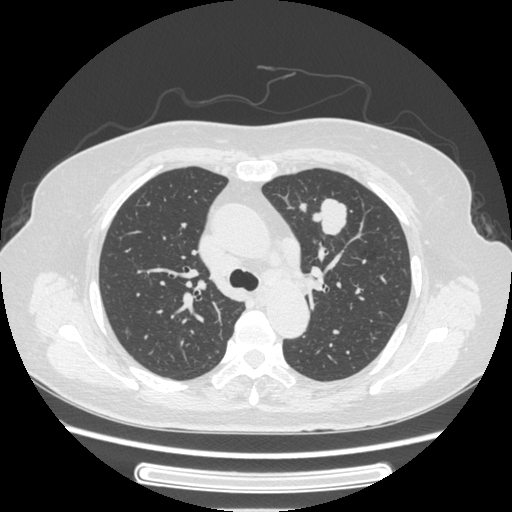
Chest CT, one axial slice. Position 165 of 227 along the scan axis. Reconstruction kernel STANDARD. 120 kVp. Lung window (W 1500 / L -600 HU). 1.25 mm slice thickness. 512 × 512 image matrix, field of view 363 × 363 mm. Female patient, age 77 years. Case-level facts recorded for this patient, not image findings: clinical TNM (as recorded): T1c N3 M0.
Outlined on this slice (bounding box drawn by a radiologist):
- lung tumour (recorded histology: adenocarcinoma): bounding box (x1, y1, x2, y2) in pixels: (312, 192, 357, 239)